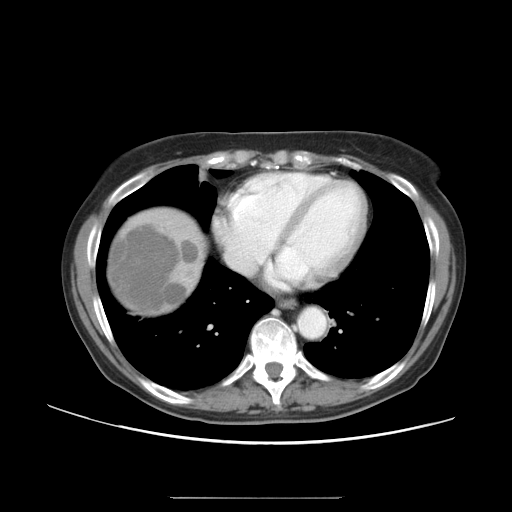
Contrast-enhanced abdominal CT, one axial slice; position 45 of 50 along the scan axis; reconstruction kernel STANDARD; intravenous contrast given; soft-tissue window (W 400 / L 40 HU); 5 mm slice thickness; 512 × 512 image matrix, field of view 389 × 389 mm. Female patient, age 58 years. Case-level facts recorded for this patient, not image findings: diagnosis: colorectal cancer liver metastases, imaged before liver resection; multiple liver metastases: yes; largest metastasis: 7.3 cm; disease in both lobes: yes.
Annotated regions visible in this slice (expert manual segmentation):
- hepatic veins: box from (x=228, y=240) to (x=255, y=269) px
- liver: (x=109, y=211)–(x=202, y=312)
- liver metastasis: (x=112, y=220)–(x=198, y=310)